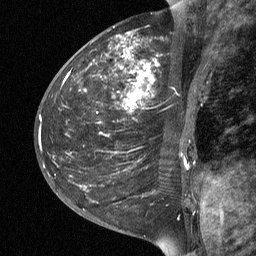
Breast MRI (dynamic contrast-enhanced), one sagittal slice; slice 21 of 64 in the series (ordered by position); dynamic contrast-enhanced study with each time point stored as its own series, time point 2 of 3 at this slice position (early post-contrast, ordered by acquisition time); 1.5 T; TE 4.8 ms, TR 27 ms; 256 × 256 image matrix. Female patient, age 42 years. From the clinical record (not read from this slice): setting: breast cancer imaged before/during neoadjuvant chemotherapy; receptor status: triple-negative.
Structures marked on this image (semi-automatically segmented with operator editing):
- analysis volume of interest (the breast-tissue region the enhancement analysis was run in; not a lesion): bounding box (x1, y1, x2, y2) in pixels: (43, 29, 203, 190)
- tumour enhancement mask (voxels above the 90 % enhancement threshold inside the analysis volume of interest): (121, 38, 155, 108)